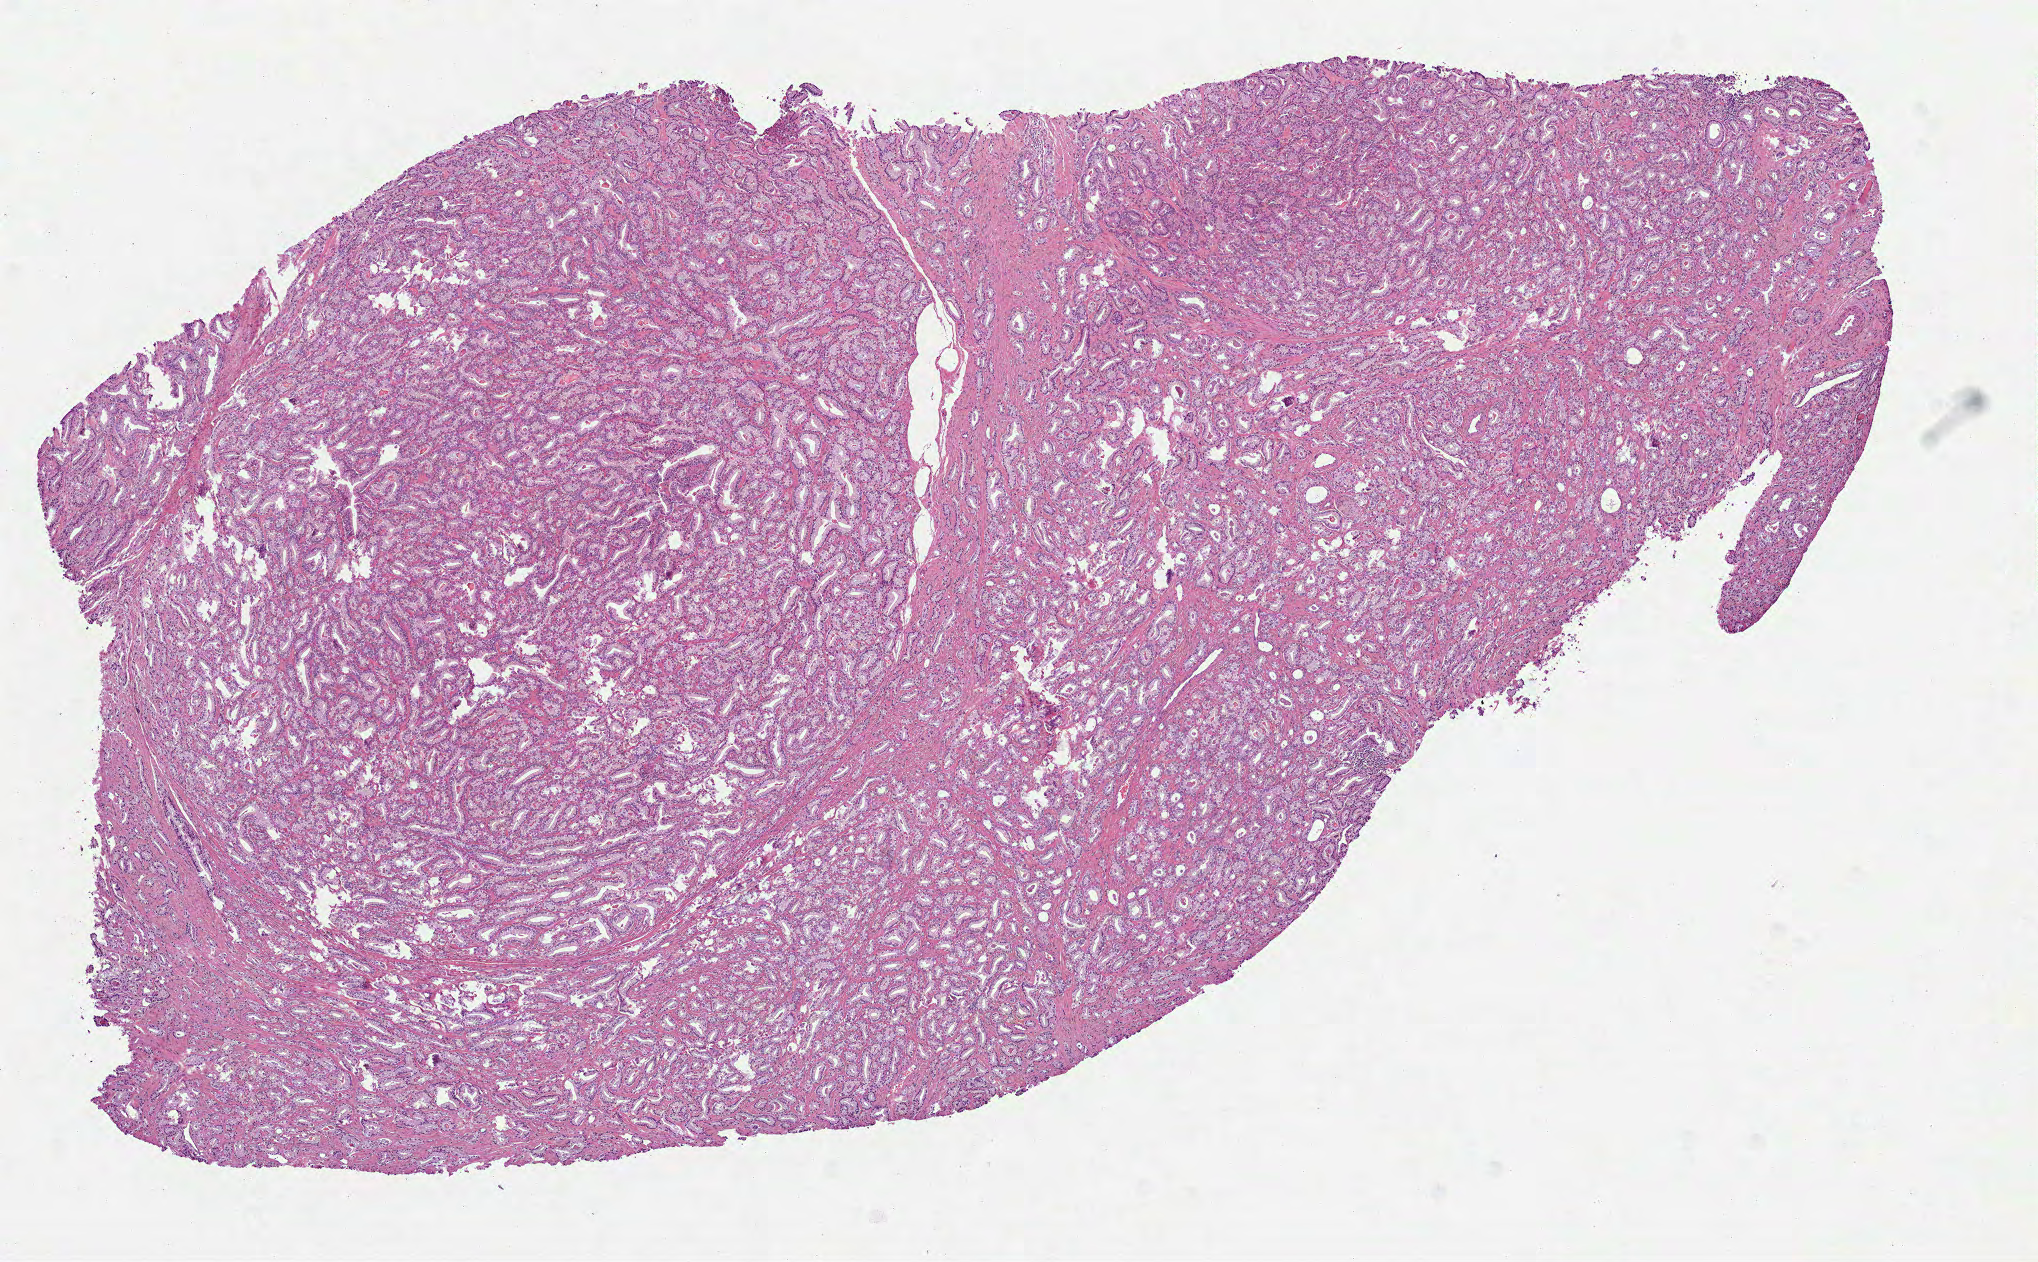
Digitized Hematoxylin and eosin (H&E) stained tissue section (whole slide) — shown as a low-resolution overview of the whole scanned area (about 8.2 x 5.1 mm, acquisition: 40x scan); FFPE section; sample: primary tumour, prostate. Male patient; age at initial diagnosis 63 years. Gleason score: 6 (3+3).
- diagnosis: Acinar cell carcinoma (prostate gland)
- laterality: right